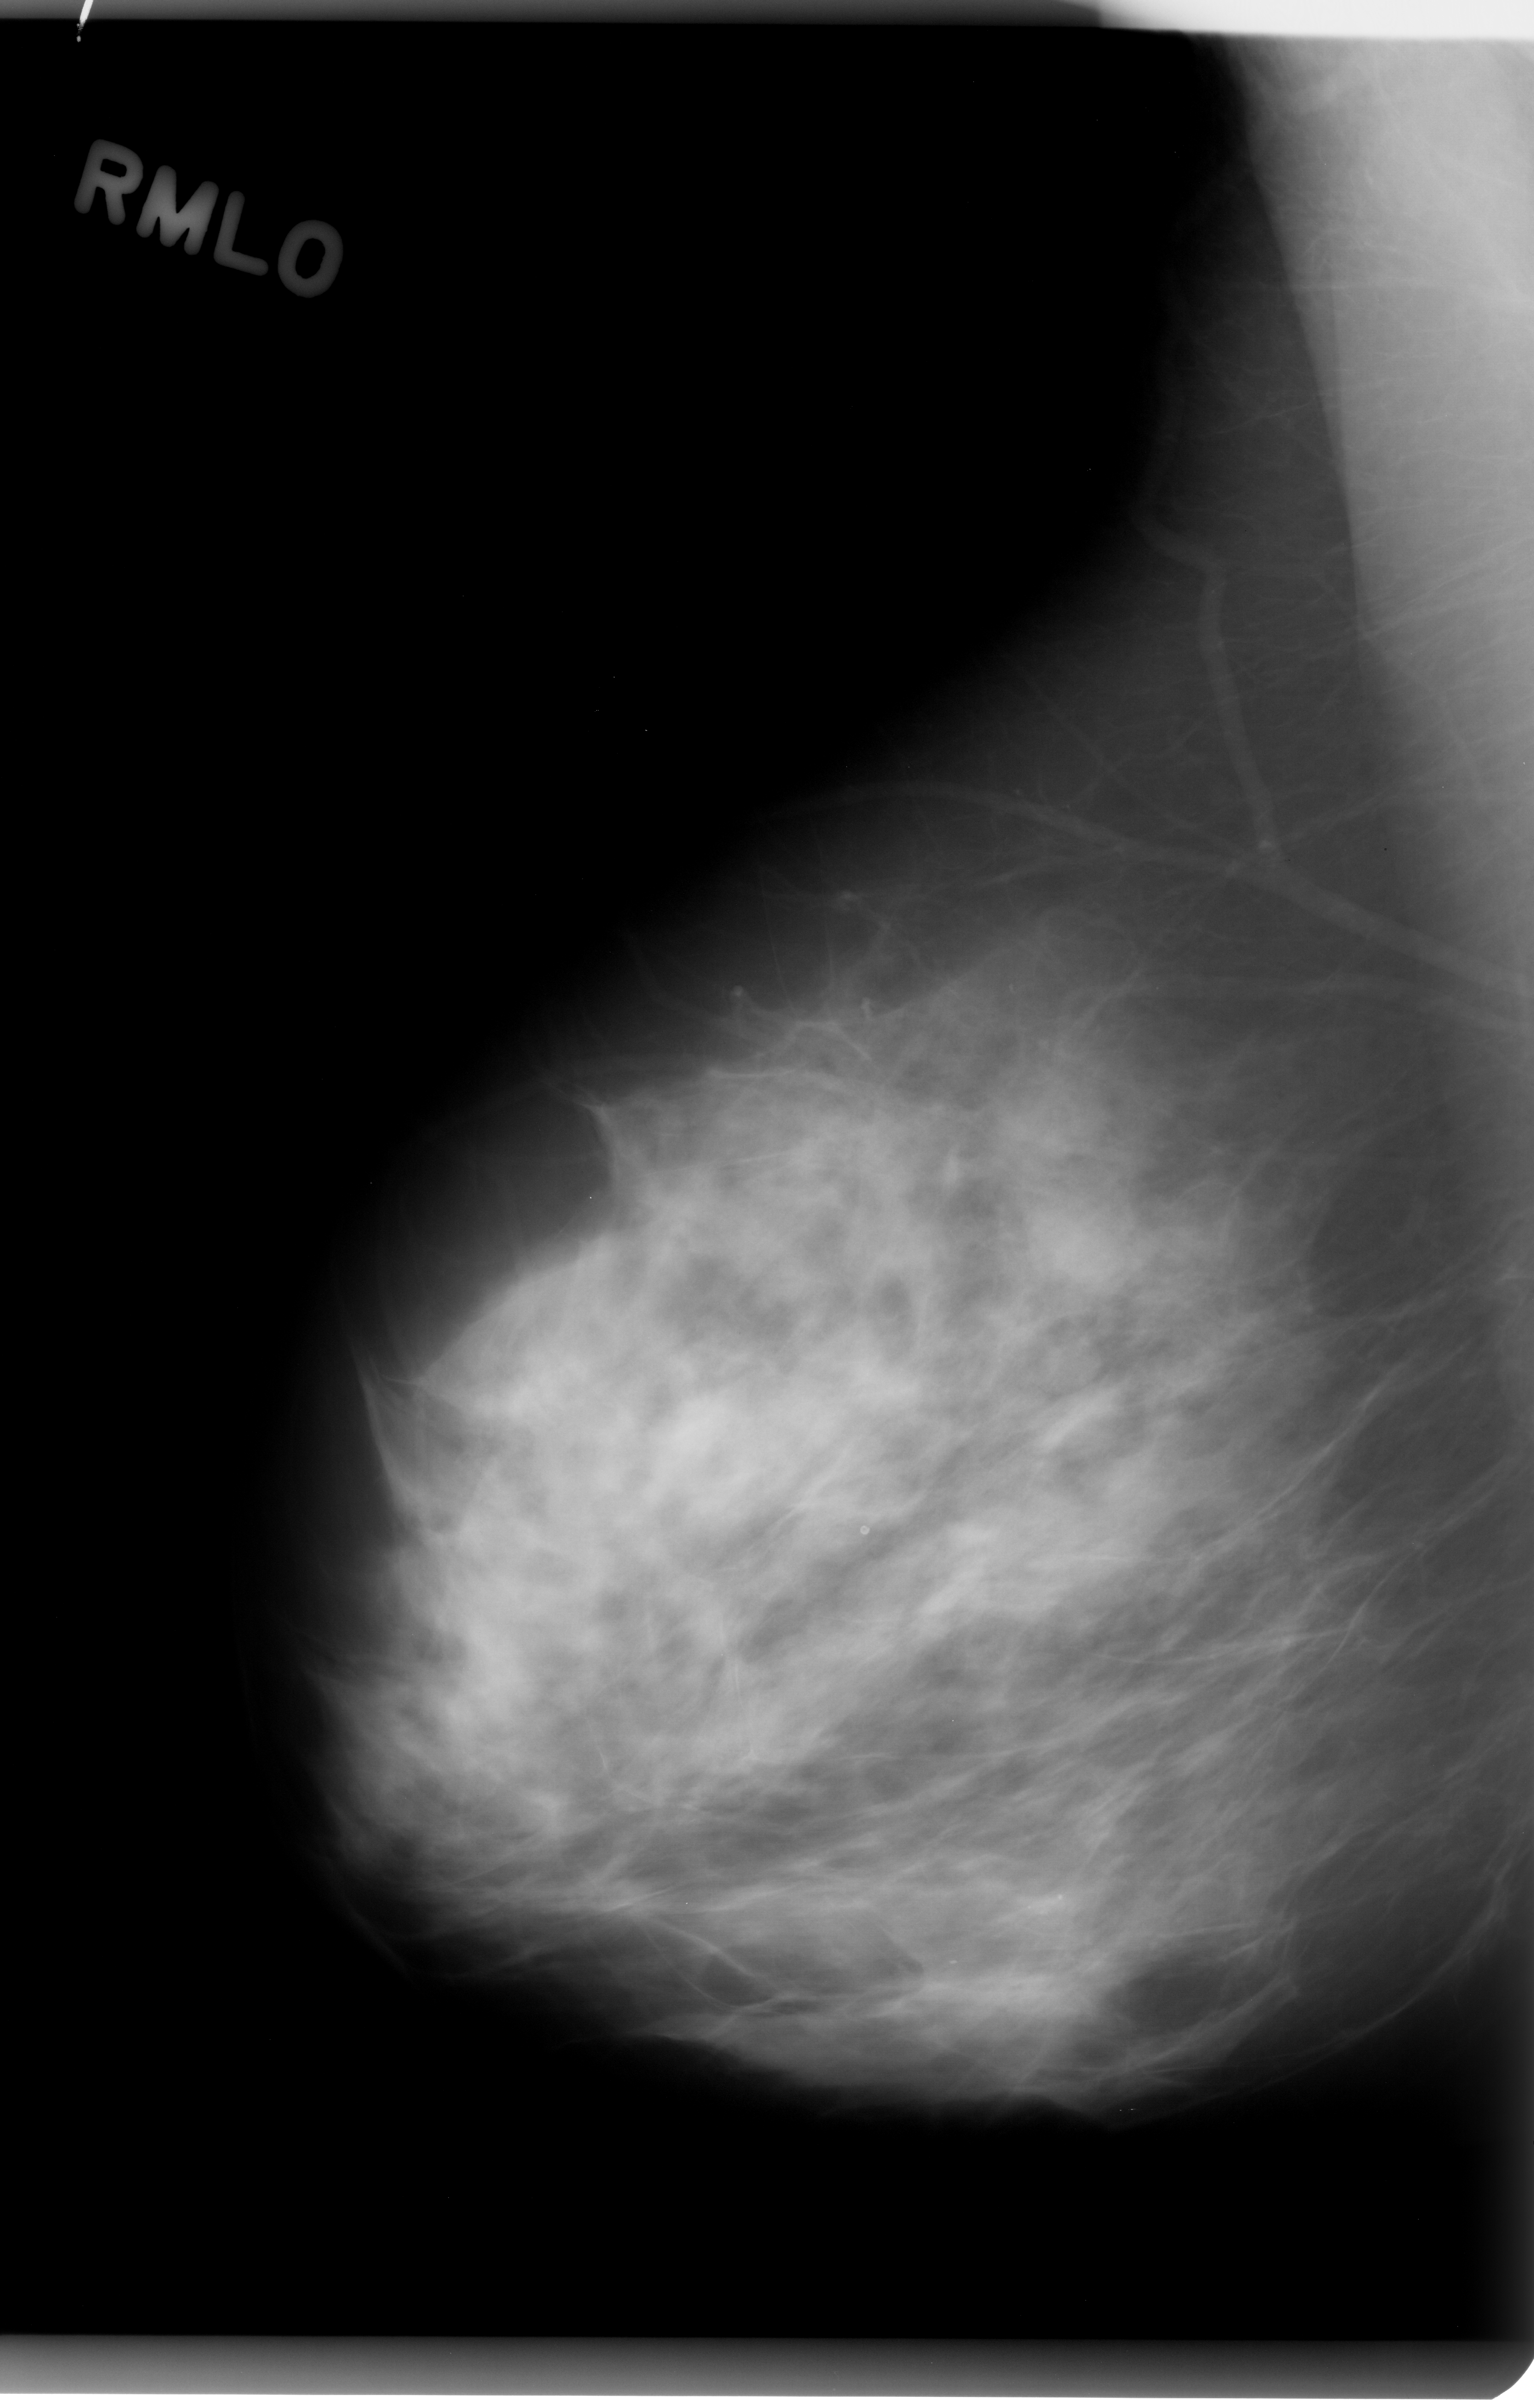
Scanned film-screen mammogram. Right breast. MLO view. 1534 × 2408 image matrix.
Expert-marked regions of interest on this film, with their recorded descriptors:
- mass, shape oval, margins microlobulated; BI-RADS assessment category 4; pathology result (as recorded, not read from the image): benign: bounding box [x1, y1, x2, y2] px = [1024, 1187, 1148, 1303]